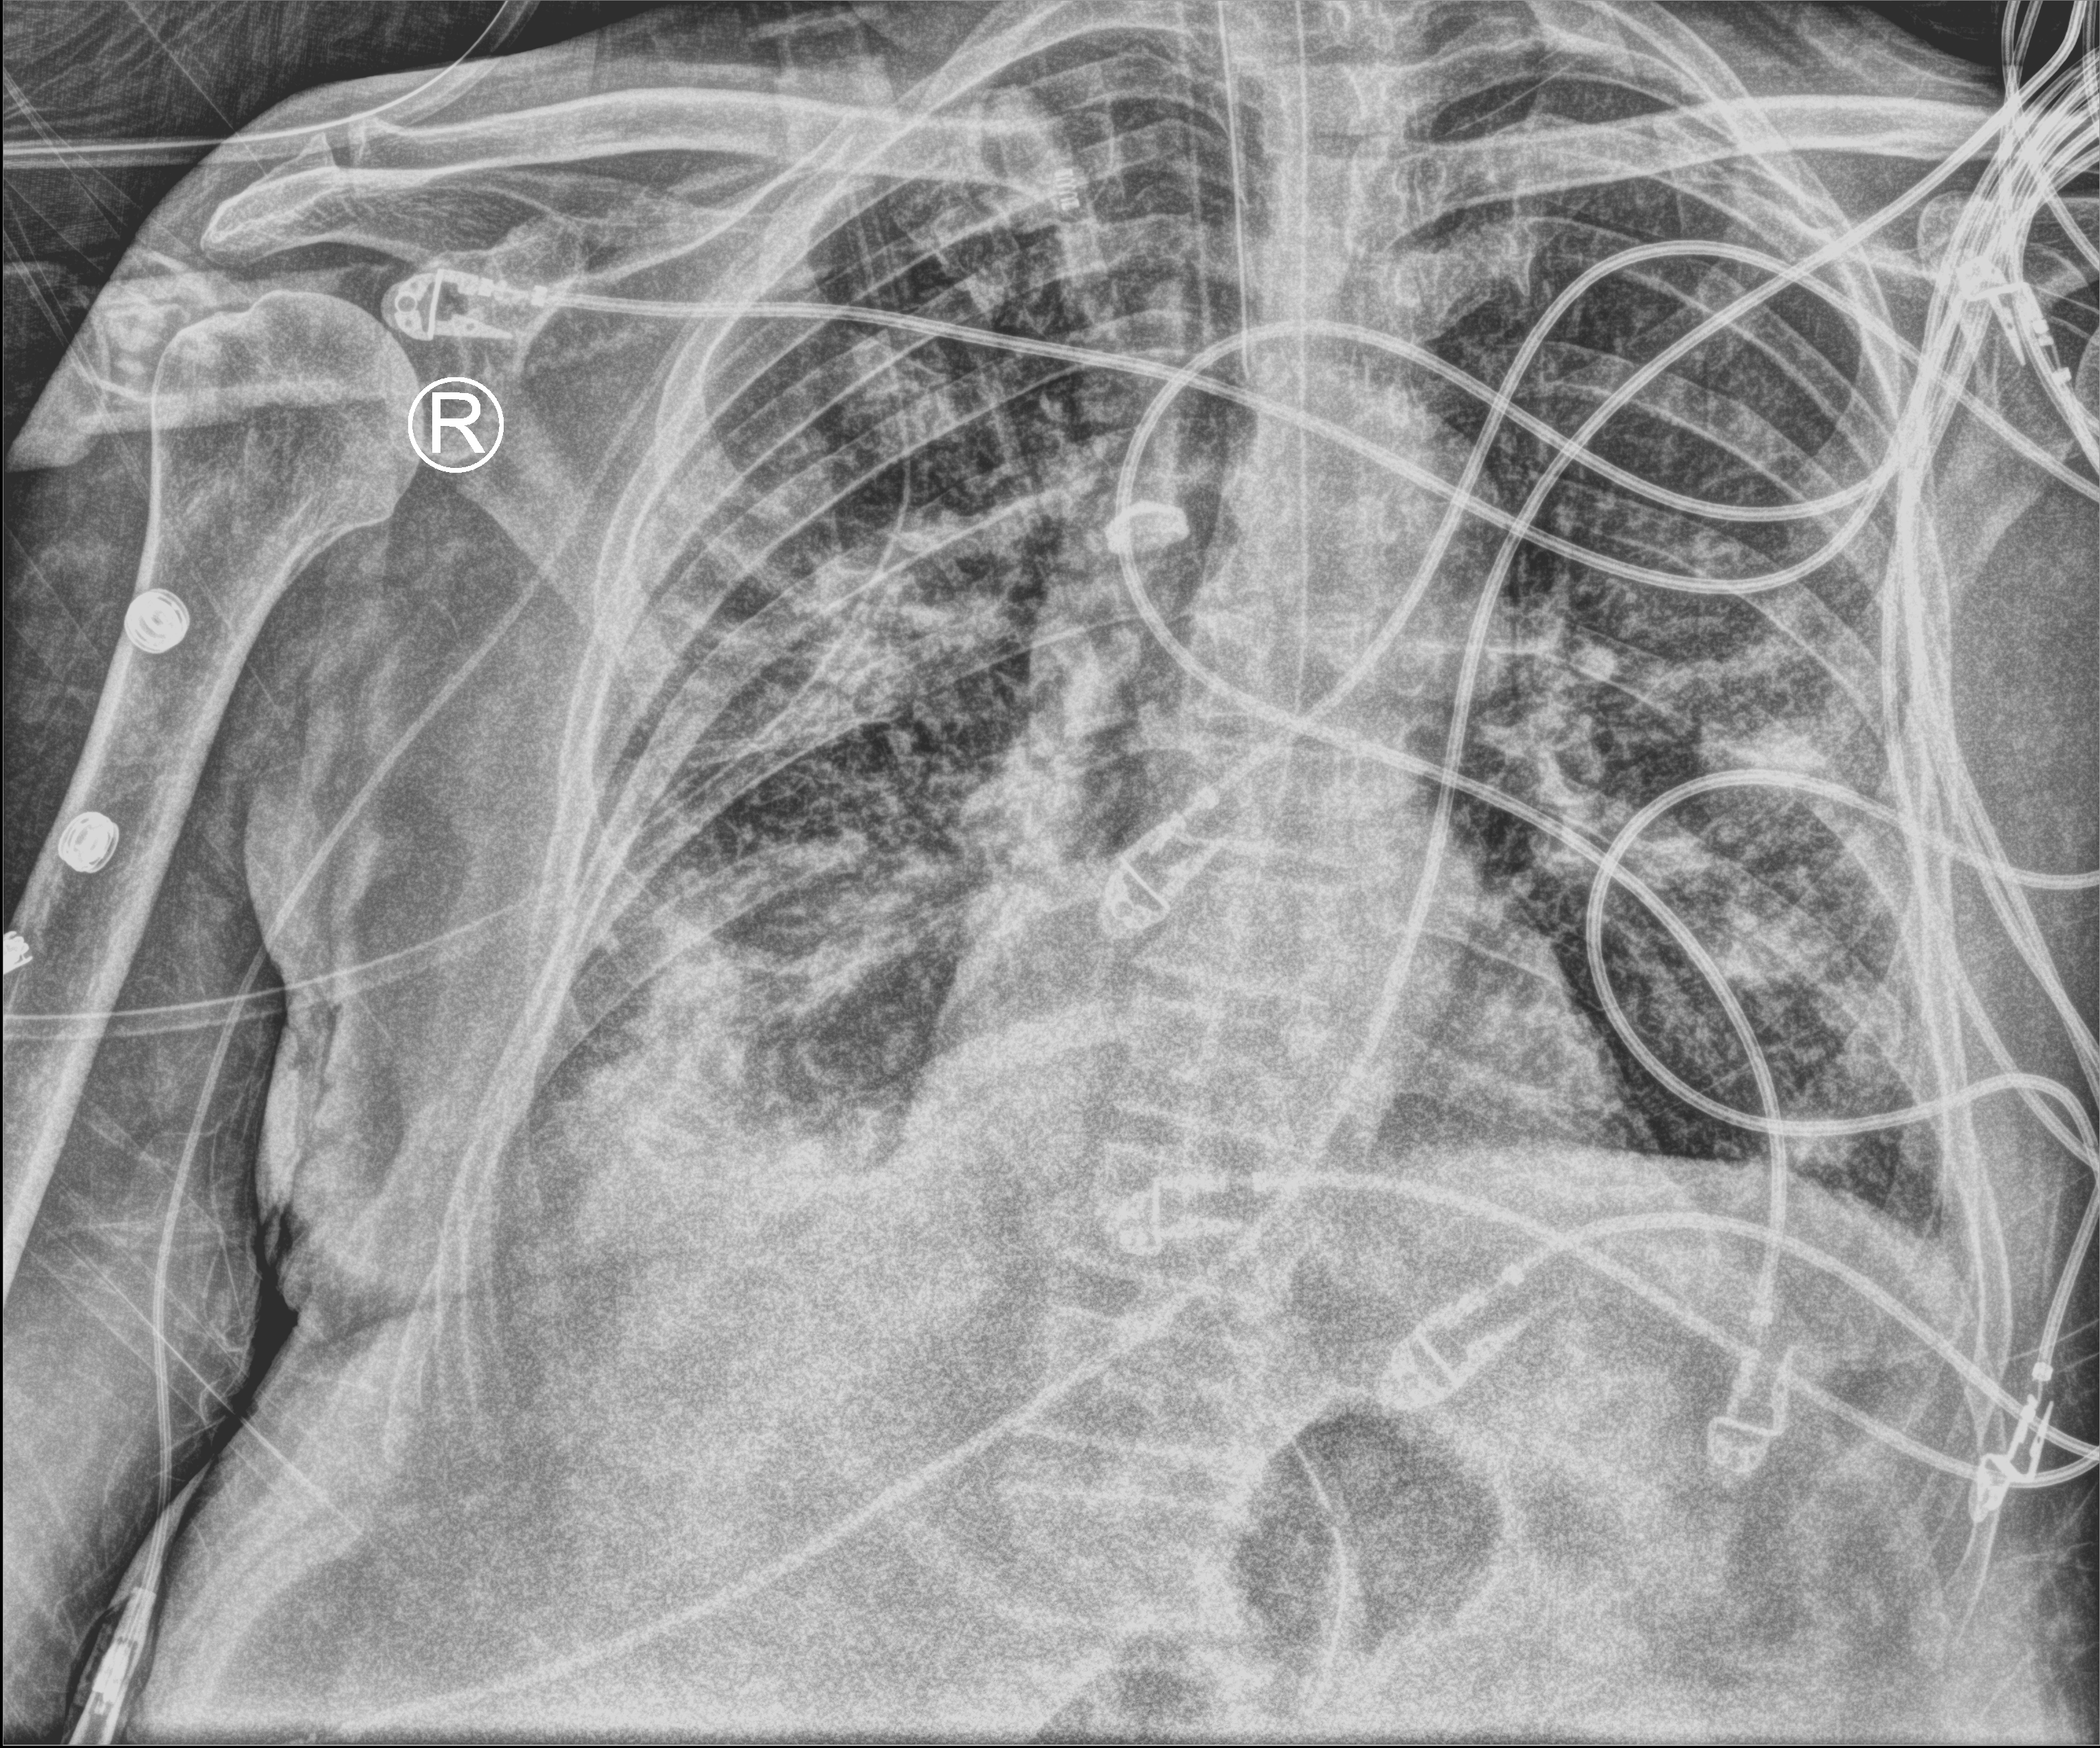
Chest X-ray (portable); anteroposterior (AP) projection. Male patient hospitalised with COVID-19, age 75–90 years.
From the hospital-stay record, not from the radiograph (when in the stay this image was taken is not recorded): admitted to intensive care during this hospital stay: yes; smoking status (admission record): never.